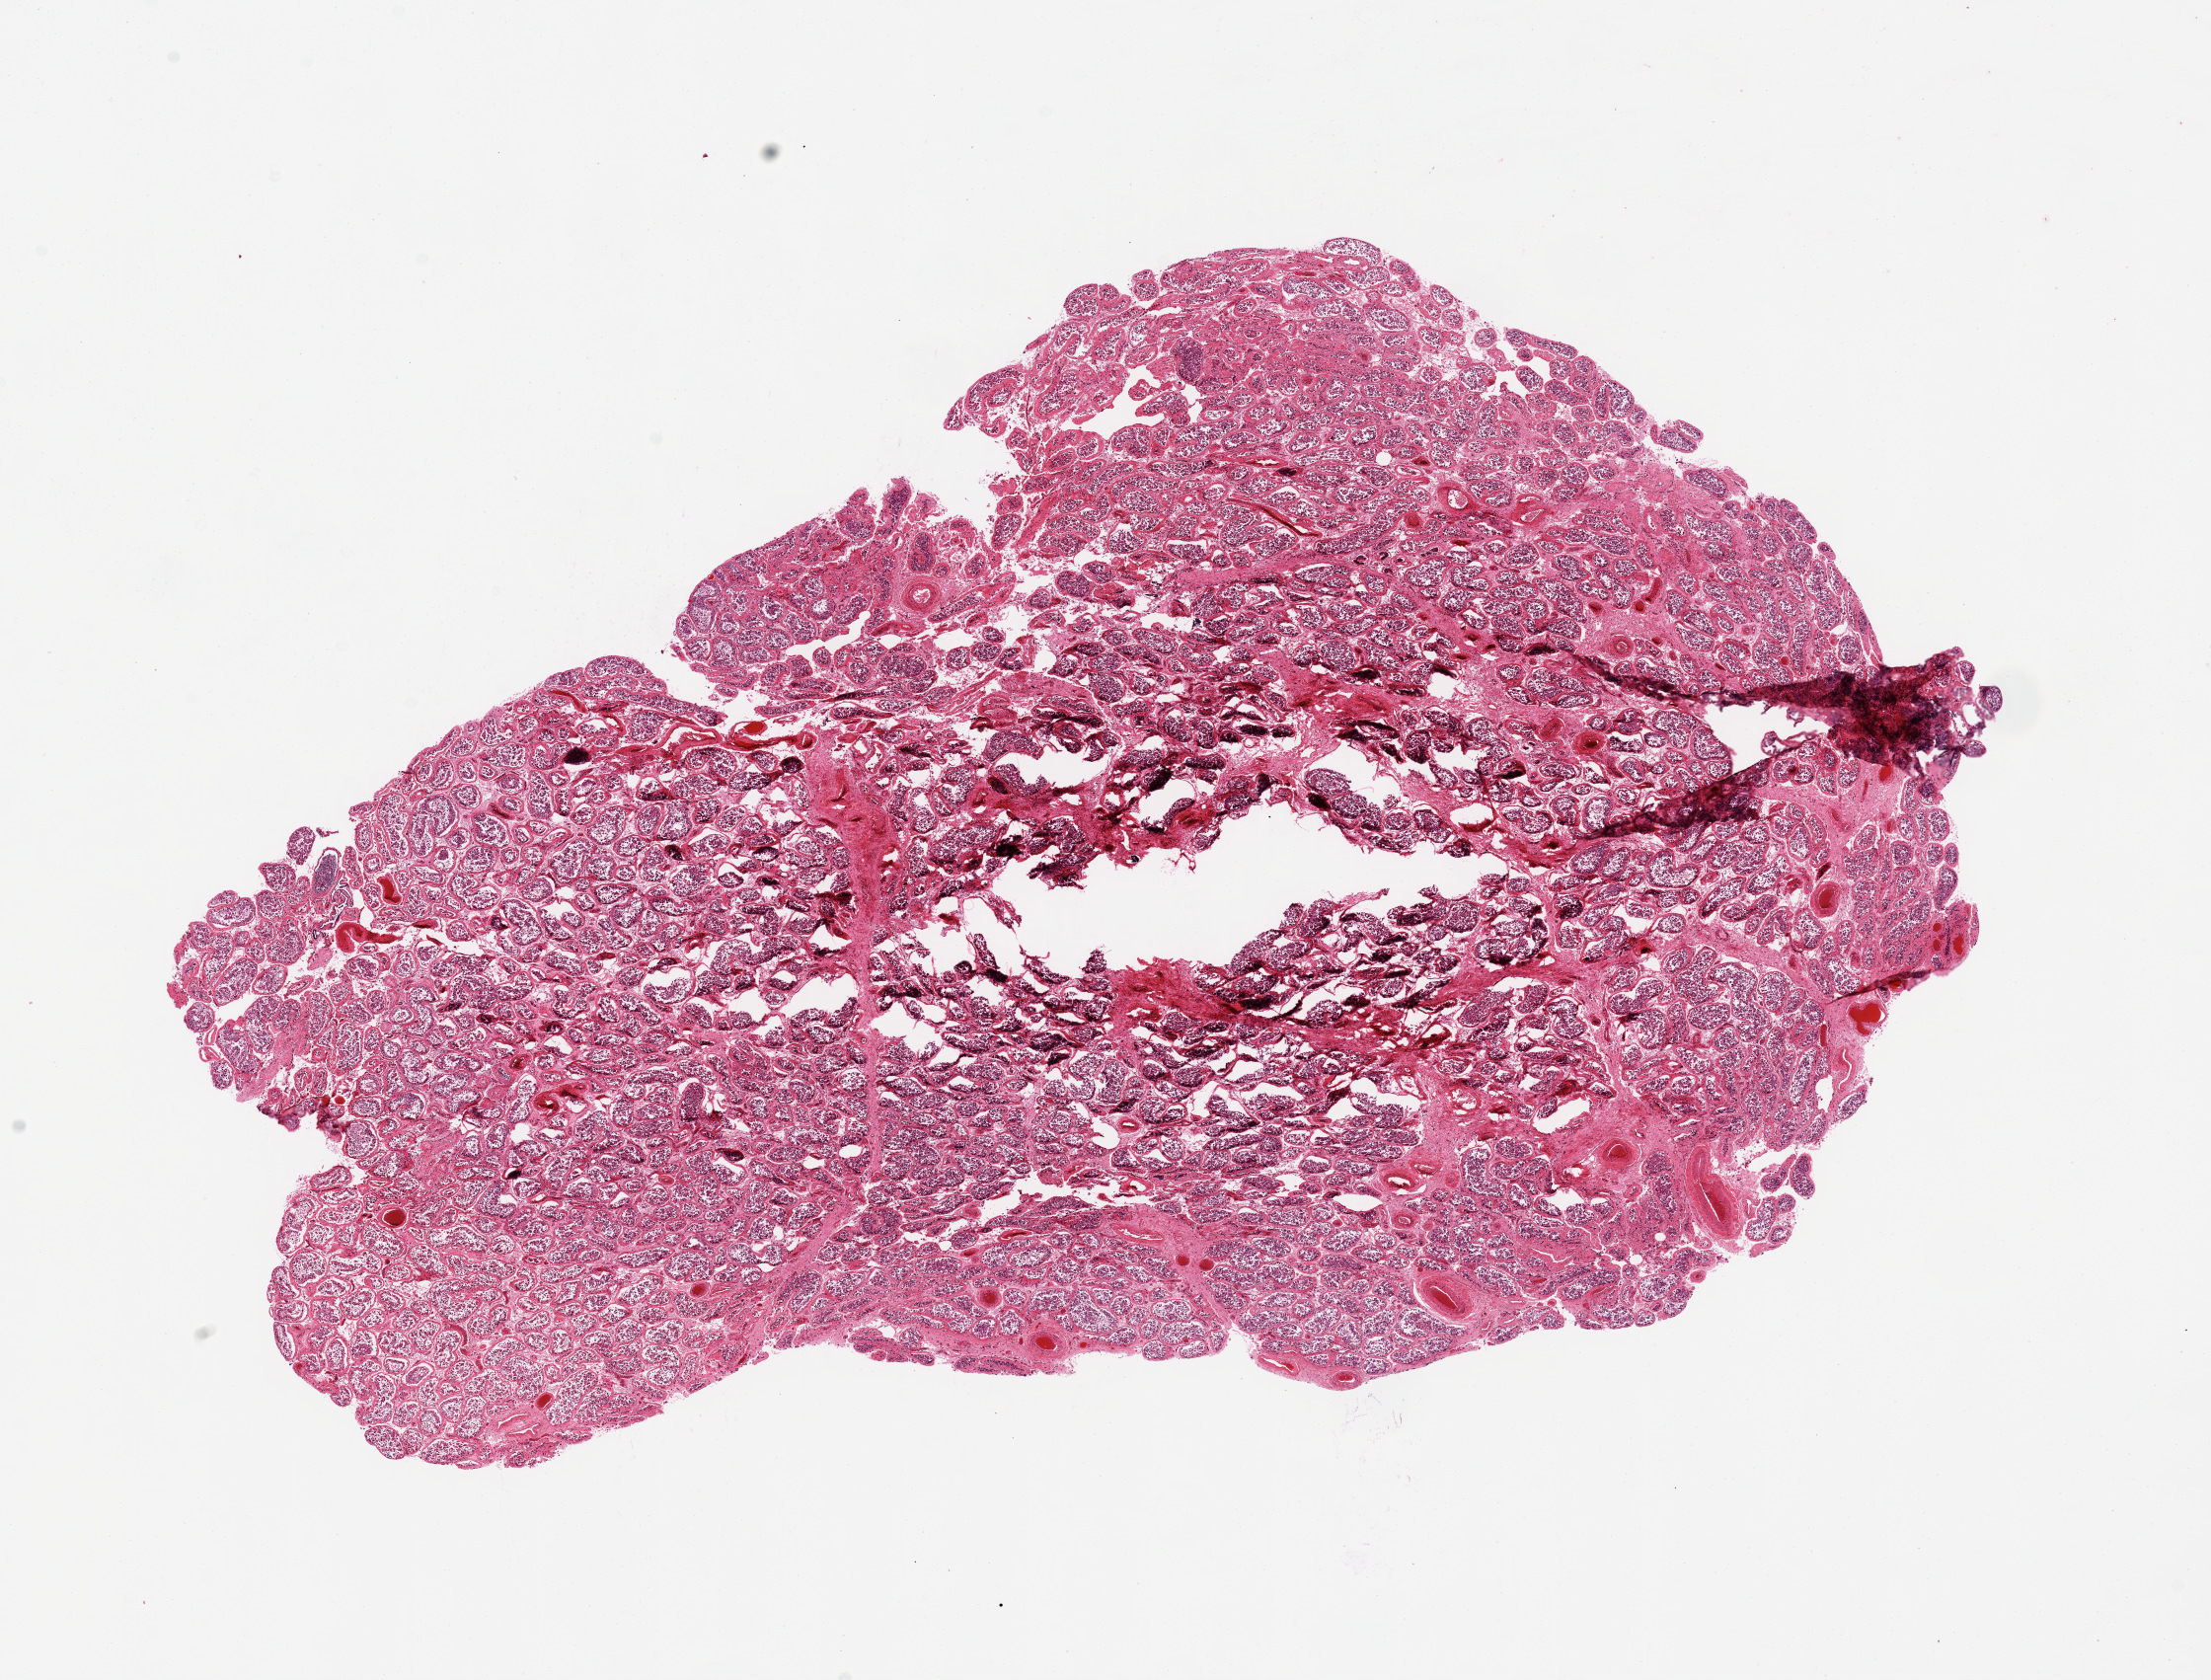
Digitized haematoxylin and eosin-stained section — whole scanned area (about 17.7 x 13.5 mm) shown as a low-resolution overview; PAXgene-fixed, paraffin-embedded tissue; sampled site (target tissue): testis; tissue donor sample. Donor sex: male.
Review note (as recorded): 13x9mm. Moderate autolysis.